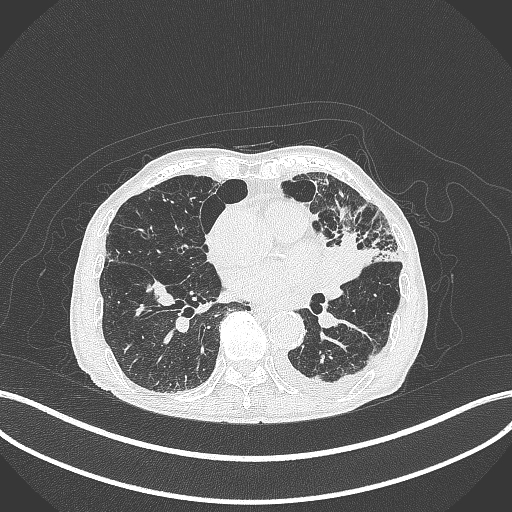
Chest CT, one axial slice; slice 170 of 385 in the series (ordered by position); lung window (W 1500 / L -600 HU); 512 × 512 image matrix, field of view 400 × 400 mm. Male patient, age 90 years or older. Case-level facts recorded for this patient, not image findings: clinical TNM (as recorded): T2b N1 M0.
Structures marked on this image (rectangle marked by the reading radiologist):
- lung tumour (recorded histology: squamous cell carcinoma): bounding box <324,239,370,284> (left, top, right, bottom; pixels)